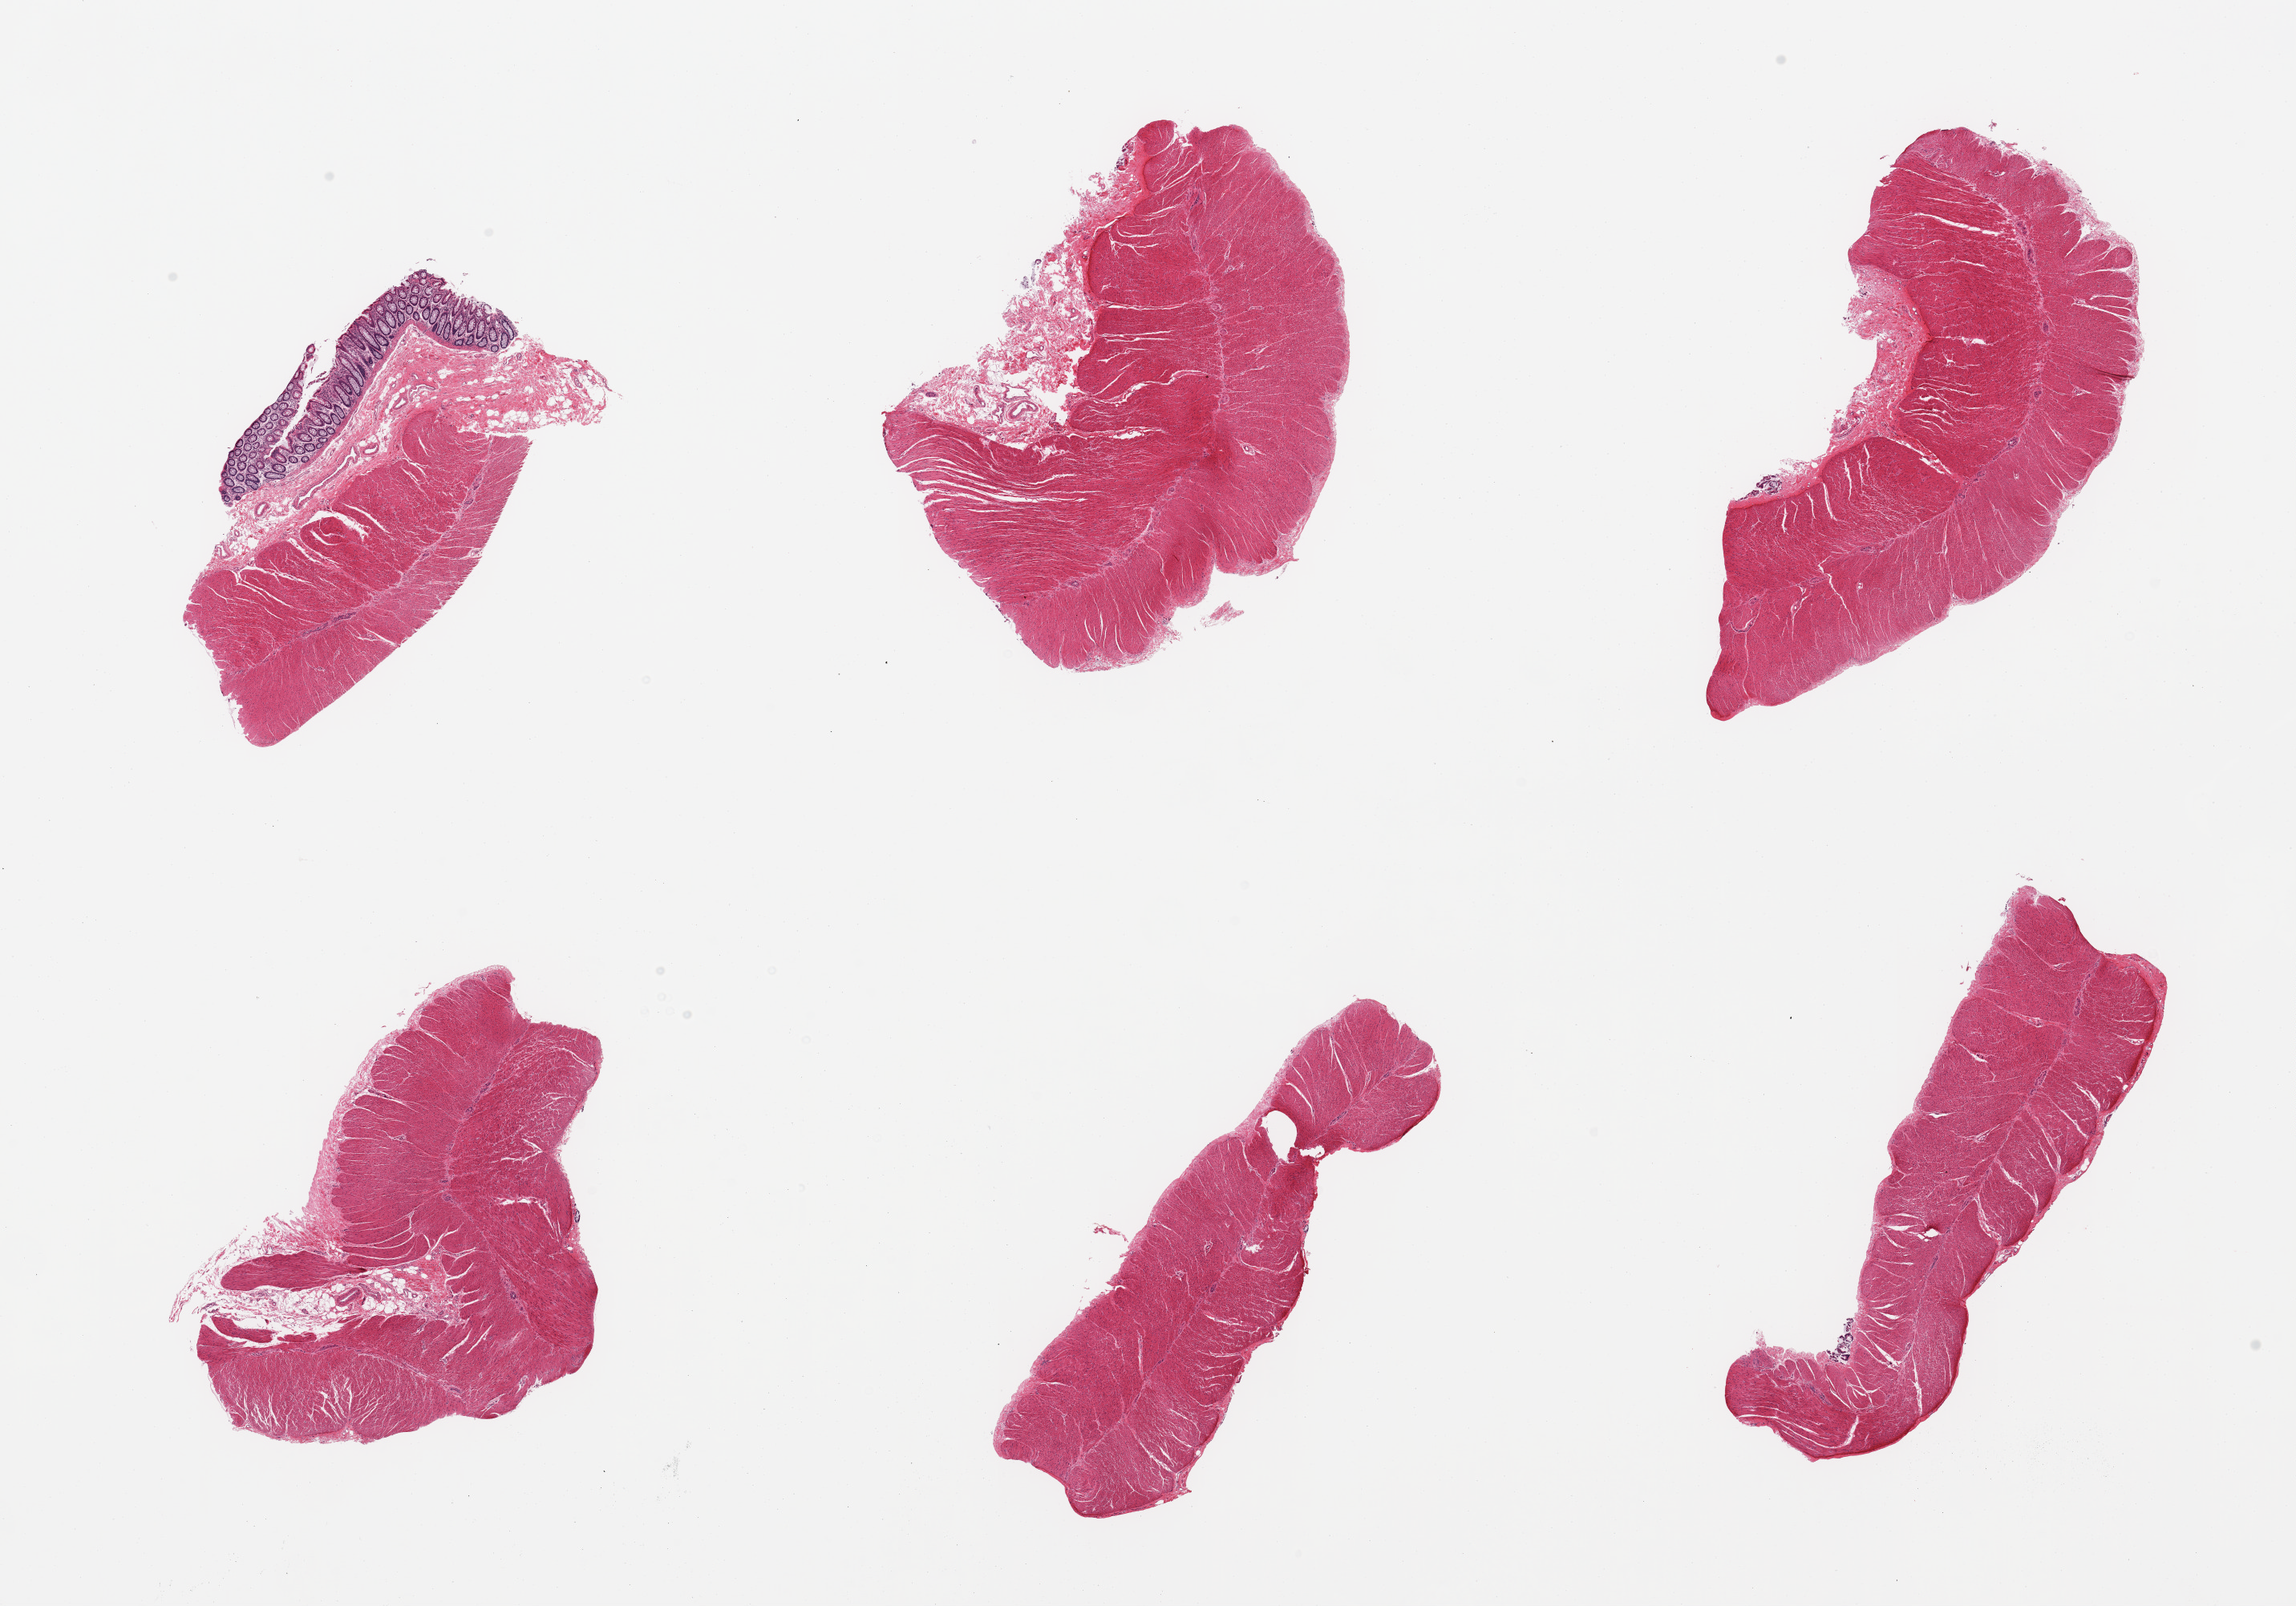
H&E whole-slide image — a low-resolution overview of the entire scanned area, about 22.6 x 15.8 mm; PAXgene-fixed paraffin-embedded (PFPE) section; target tissue: sigmoid colon; tissue donor sample. Donor: male.
Pathologist's review note for this sample: 6 pieces: one contains mucosa [not target] labeled, as well as muscularis; others are well dissected muscularis propria (target).